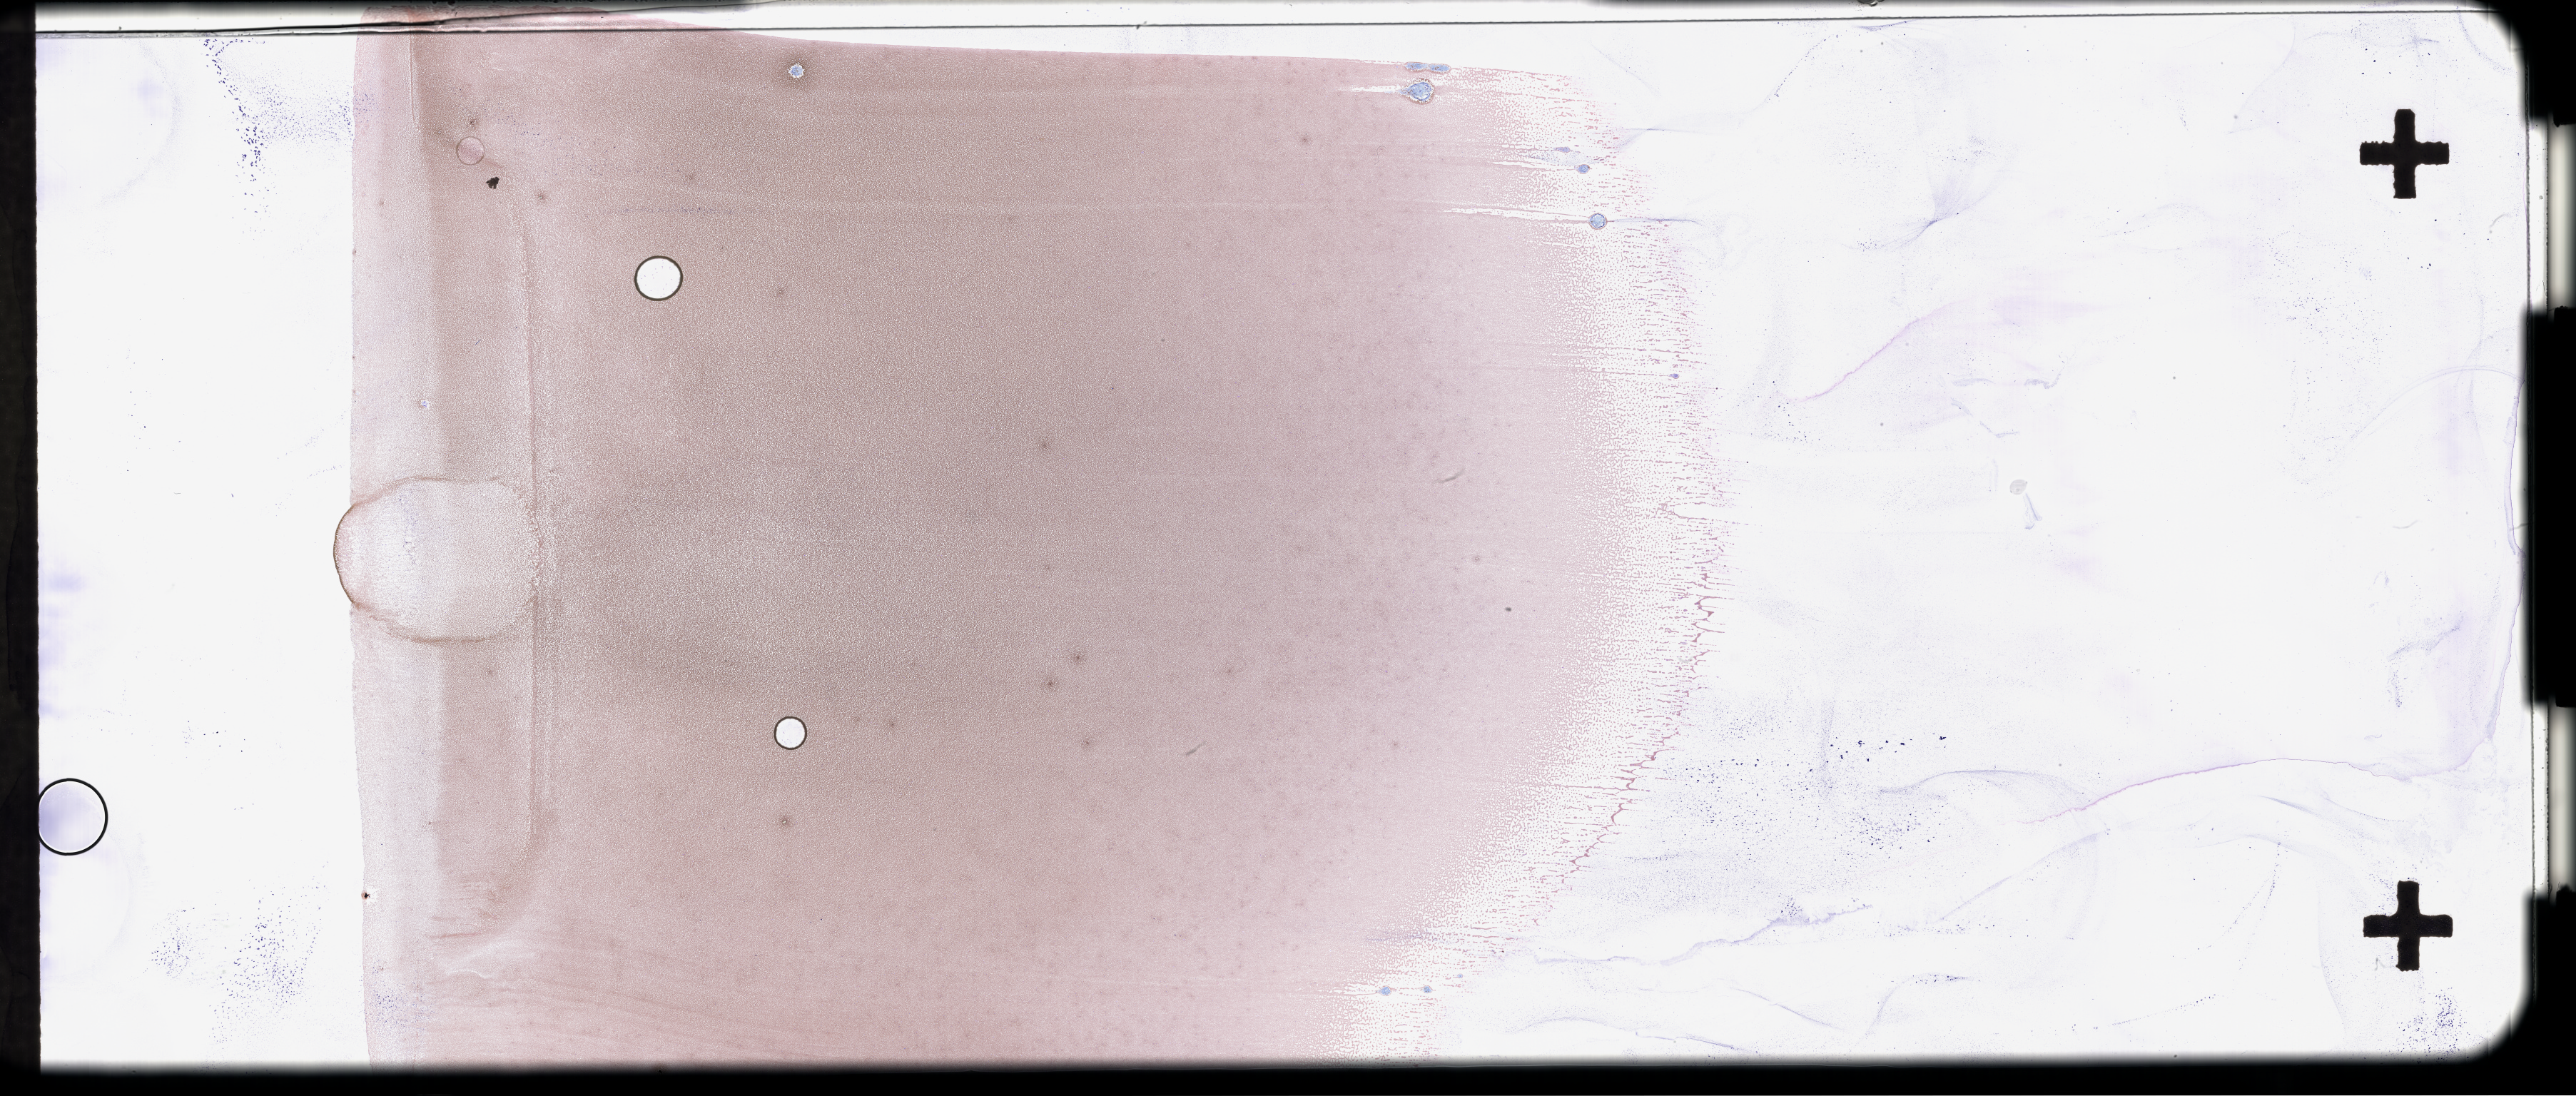
Wright–Giemsa-stained whole blood smear, whole-slide image, low-resolution overview of the scanned area, about 58.3 x 24.8 mm; smear from an EDTA sample; collected at baseline (before treatment). Patient sex: female.
* from a patient with: Plasma Cell Myeloma